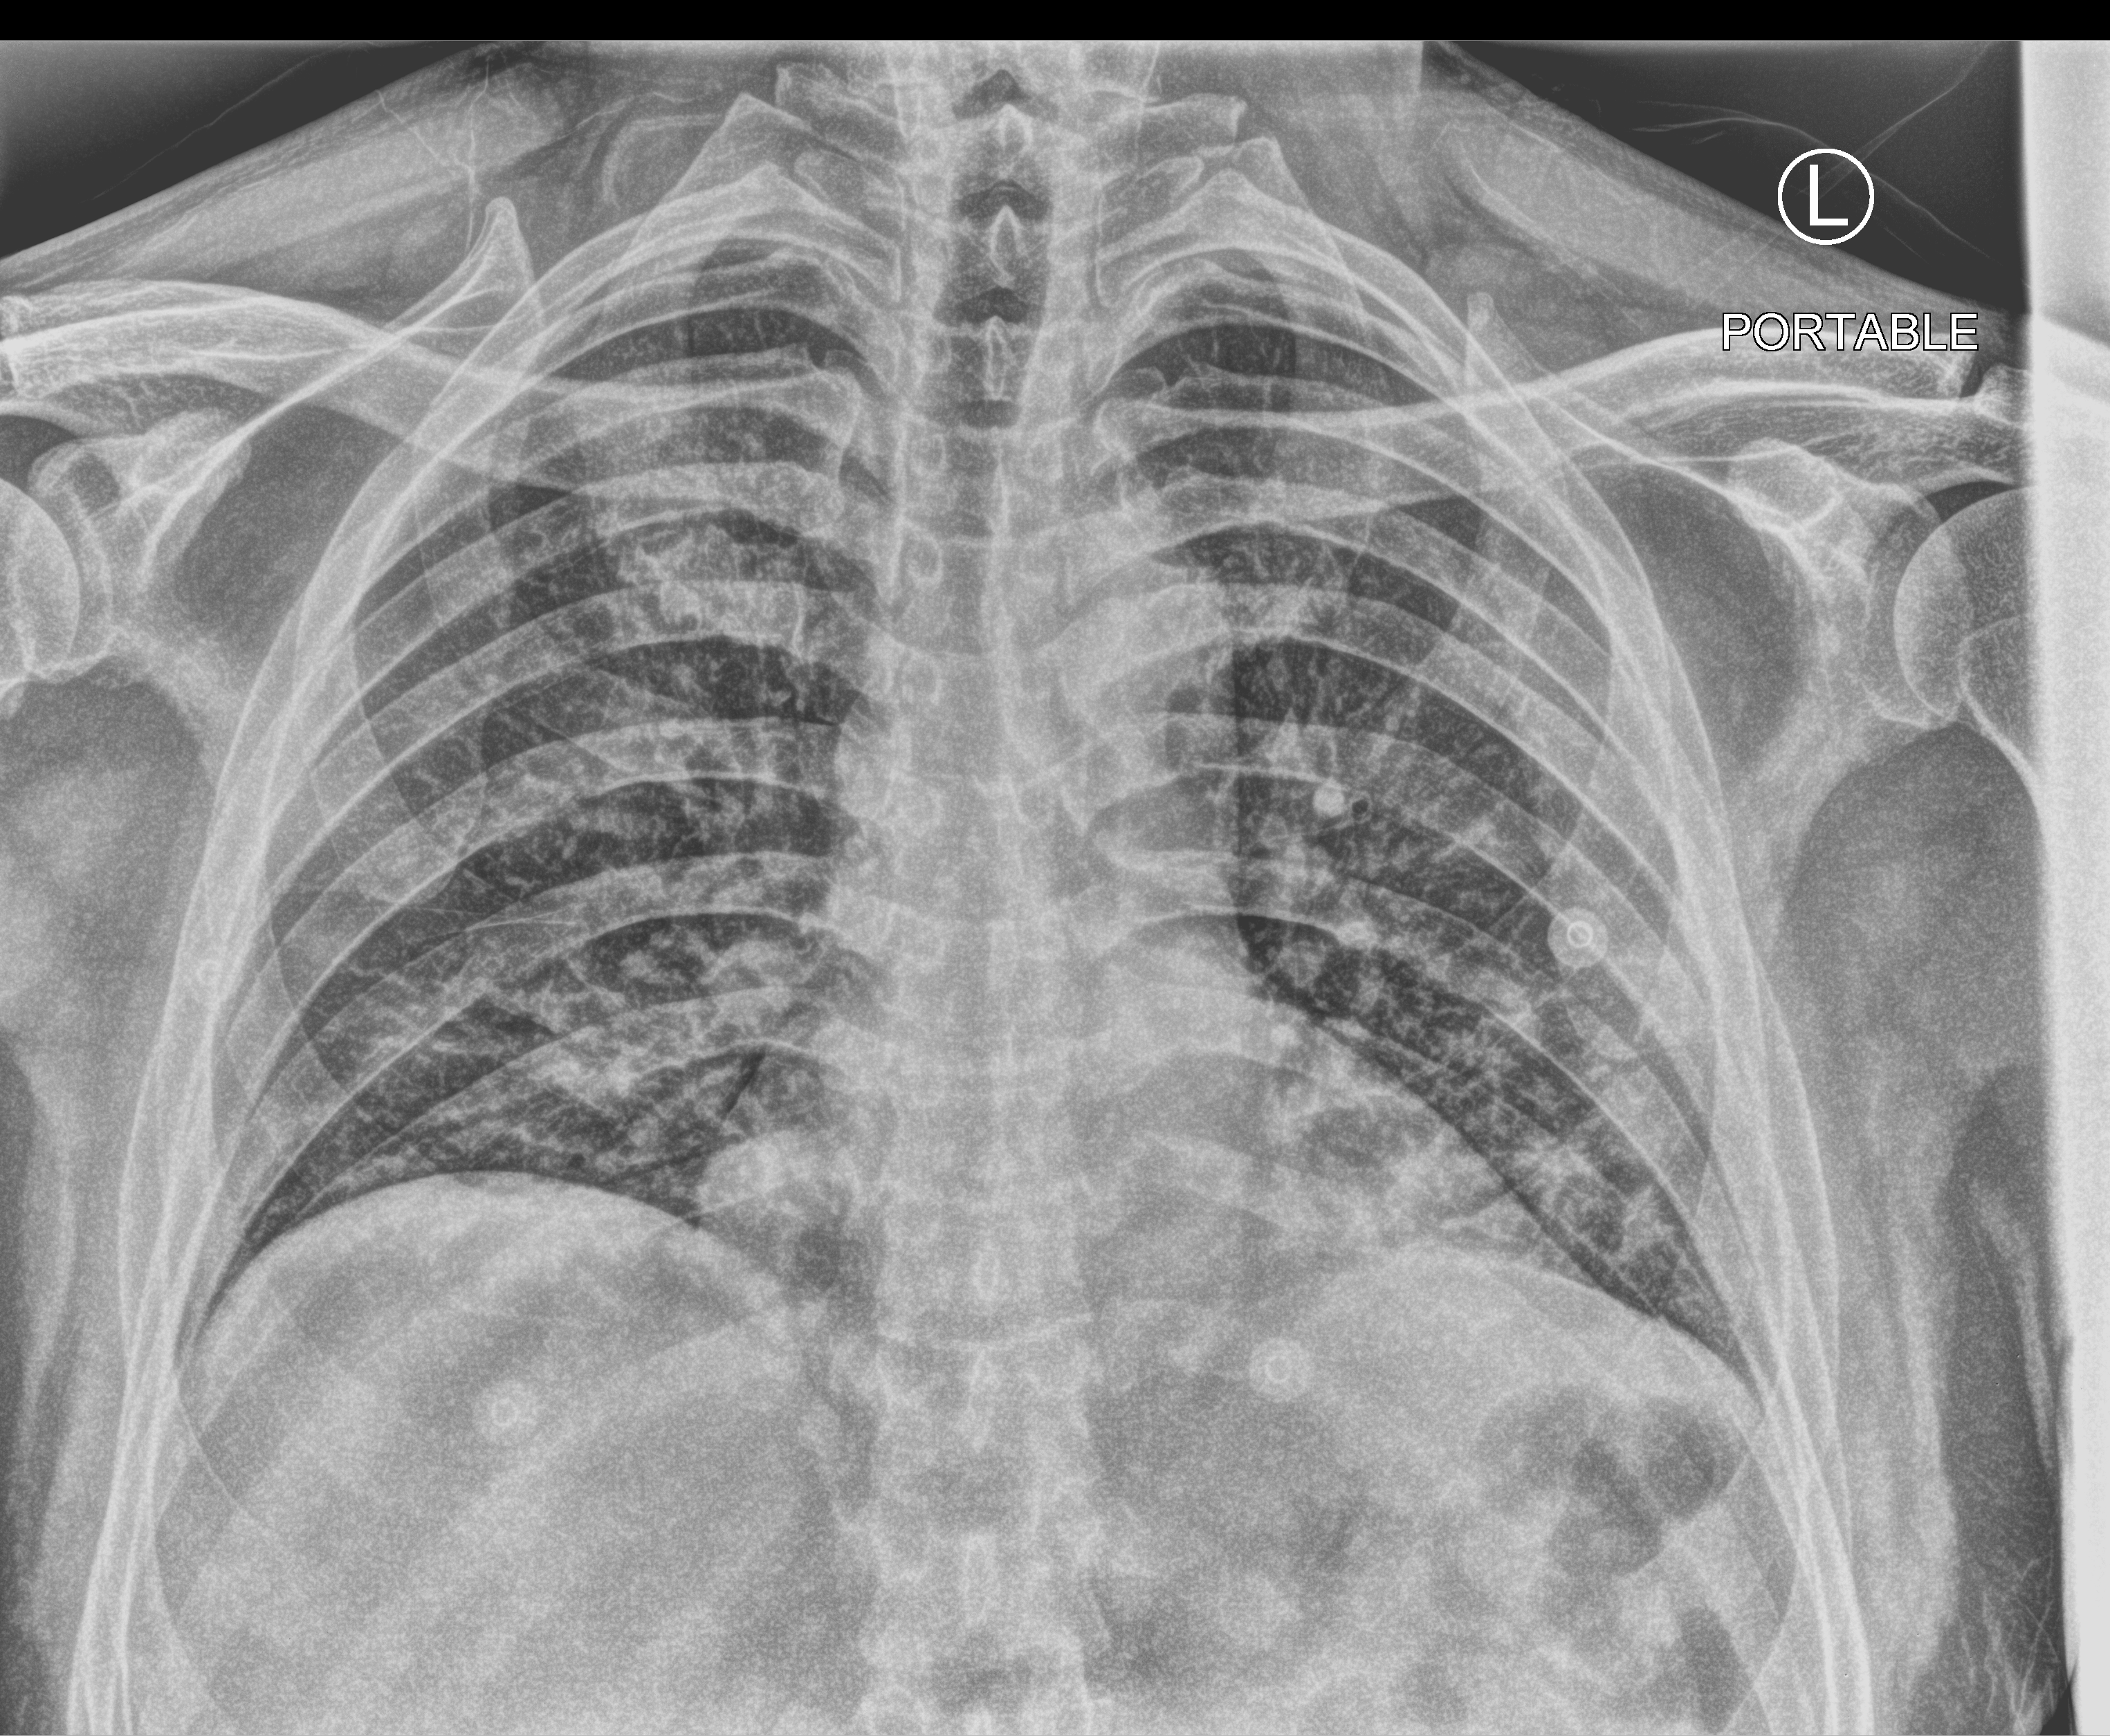
Portable chest radiograph. Male patient hospitalised with COVID-19, age 18–59 years.
Hospital-stay facts (about this admission, not read from this image; timing relative to this image not recorded):
- mechanically ventilated during this hospital stay: no
- admitted to intensive care during this hospital stay: no